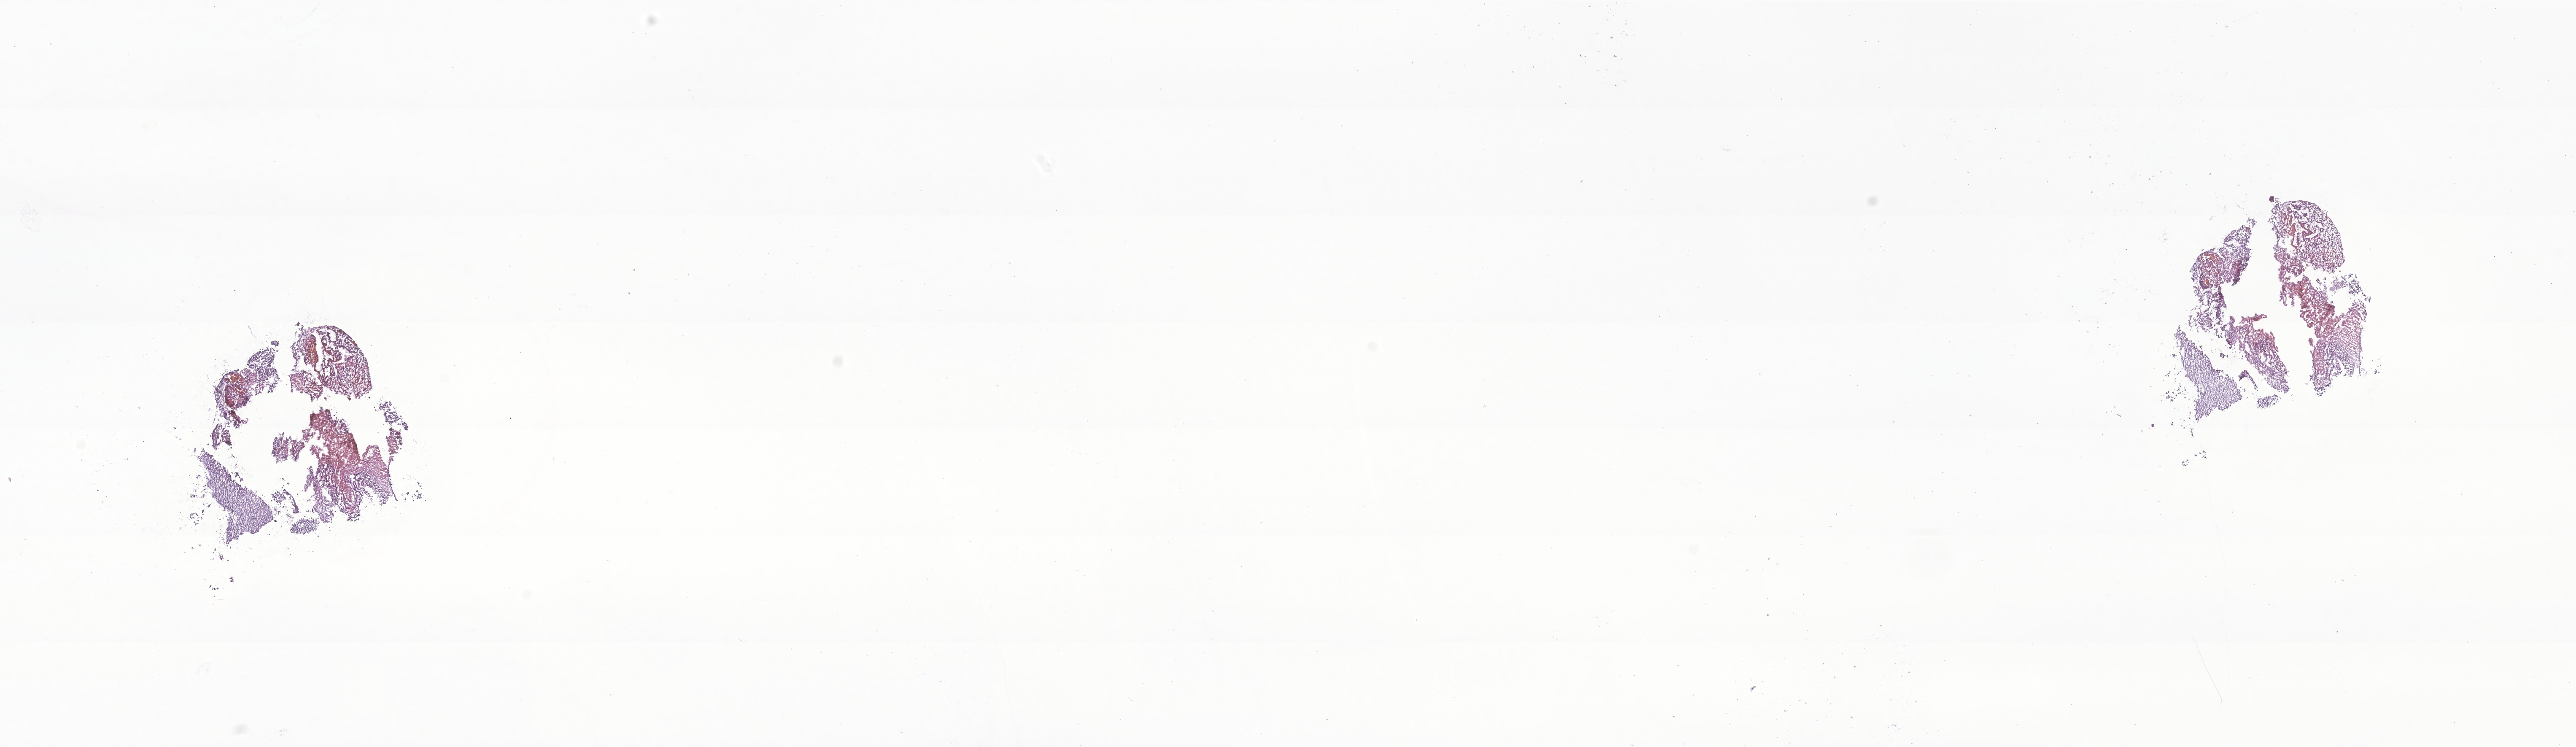
Hematoxylin and eosin (H&E) whole-slide image of tumor tissue from the brain, low-resolution overview of the scanned area, about 25.8 x 7.5 mm. Frozen section (OCT-embedded). Male patient, age 416 days (about 1.1 years).
* diagnosis (ICD-O-3 morphology term): Atypical teratoid/rhabdoid tumor